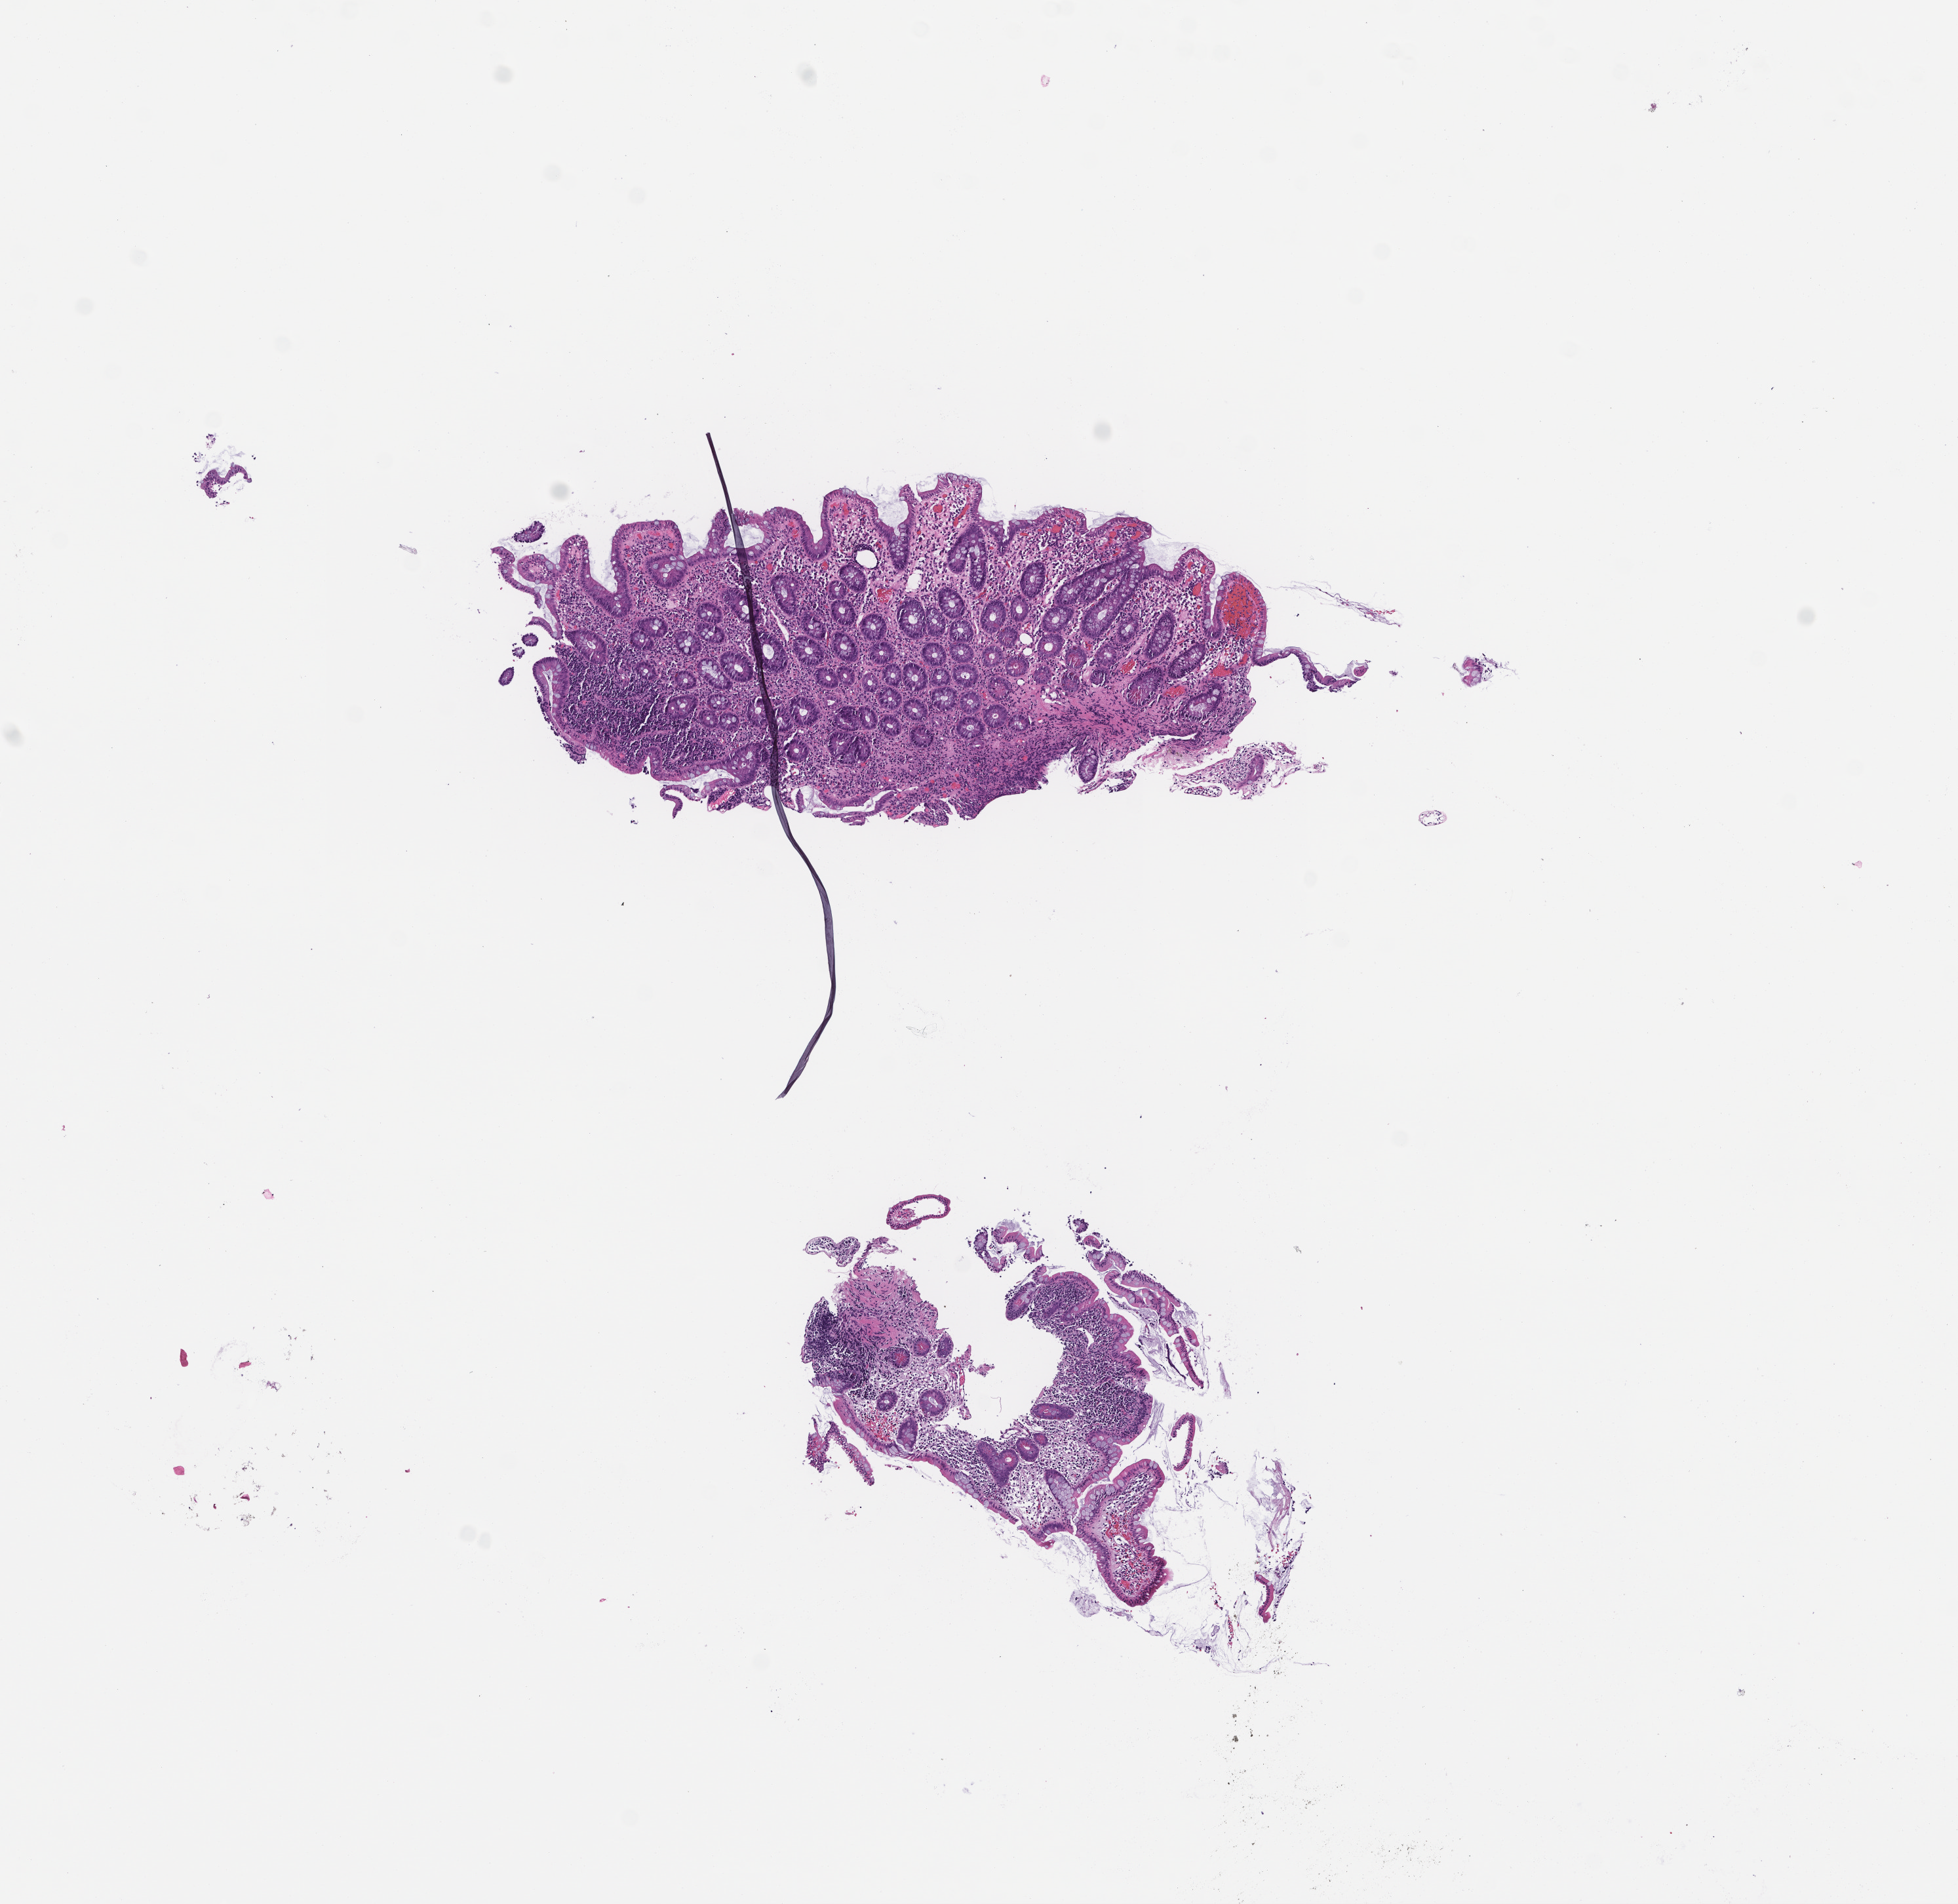
Whole-slide image, haematoxylin and eosin stain — whole scanned area (about 6.0 x 5.9 mm) shown as a low-resolution overview, formalin-fixed paraffin-embedded section, tissue site: colon, specimen time point: archival tissue. Patient sex: male.
This section: primary tumour tissue. Diagnosis: Colorectal Carcinoma.